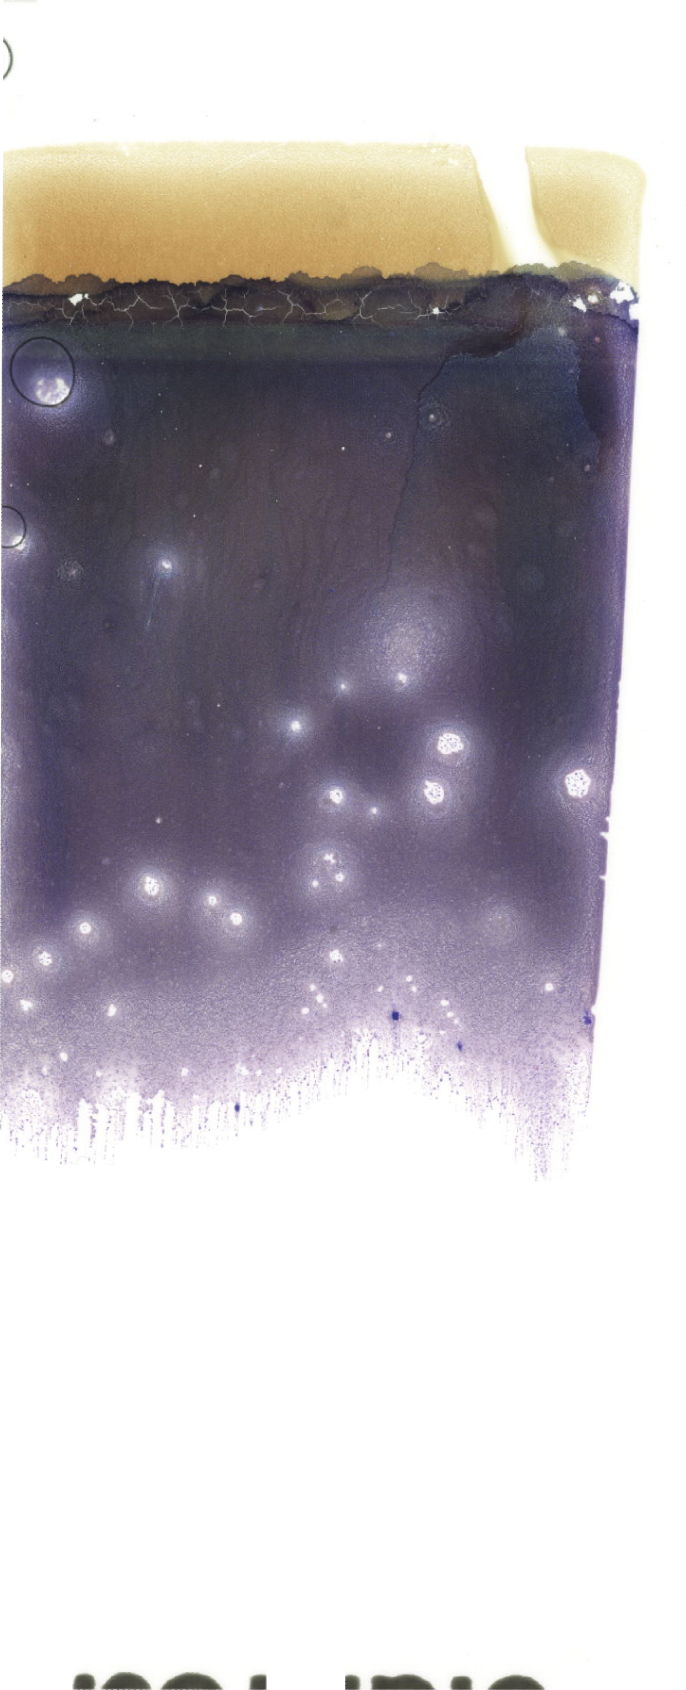
Bone marrow aspirate smear, May-Grünwald-Giemsa (MGG) stain, whole-slide image — a low-resolution overview of the entire scanned area, about 19.4 x 47.9 mm. Female patient.
Diagnosis: Acute Promyelocytic Leukemia with t(15;17)(q24.1;q21.2);PML-RARA.